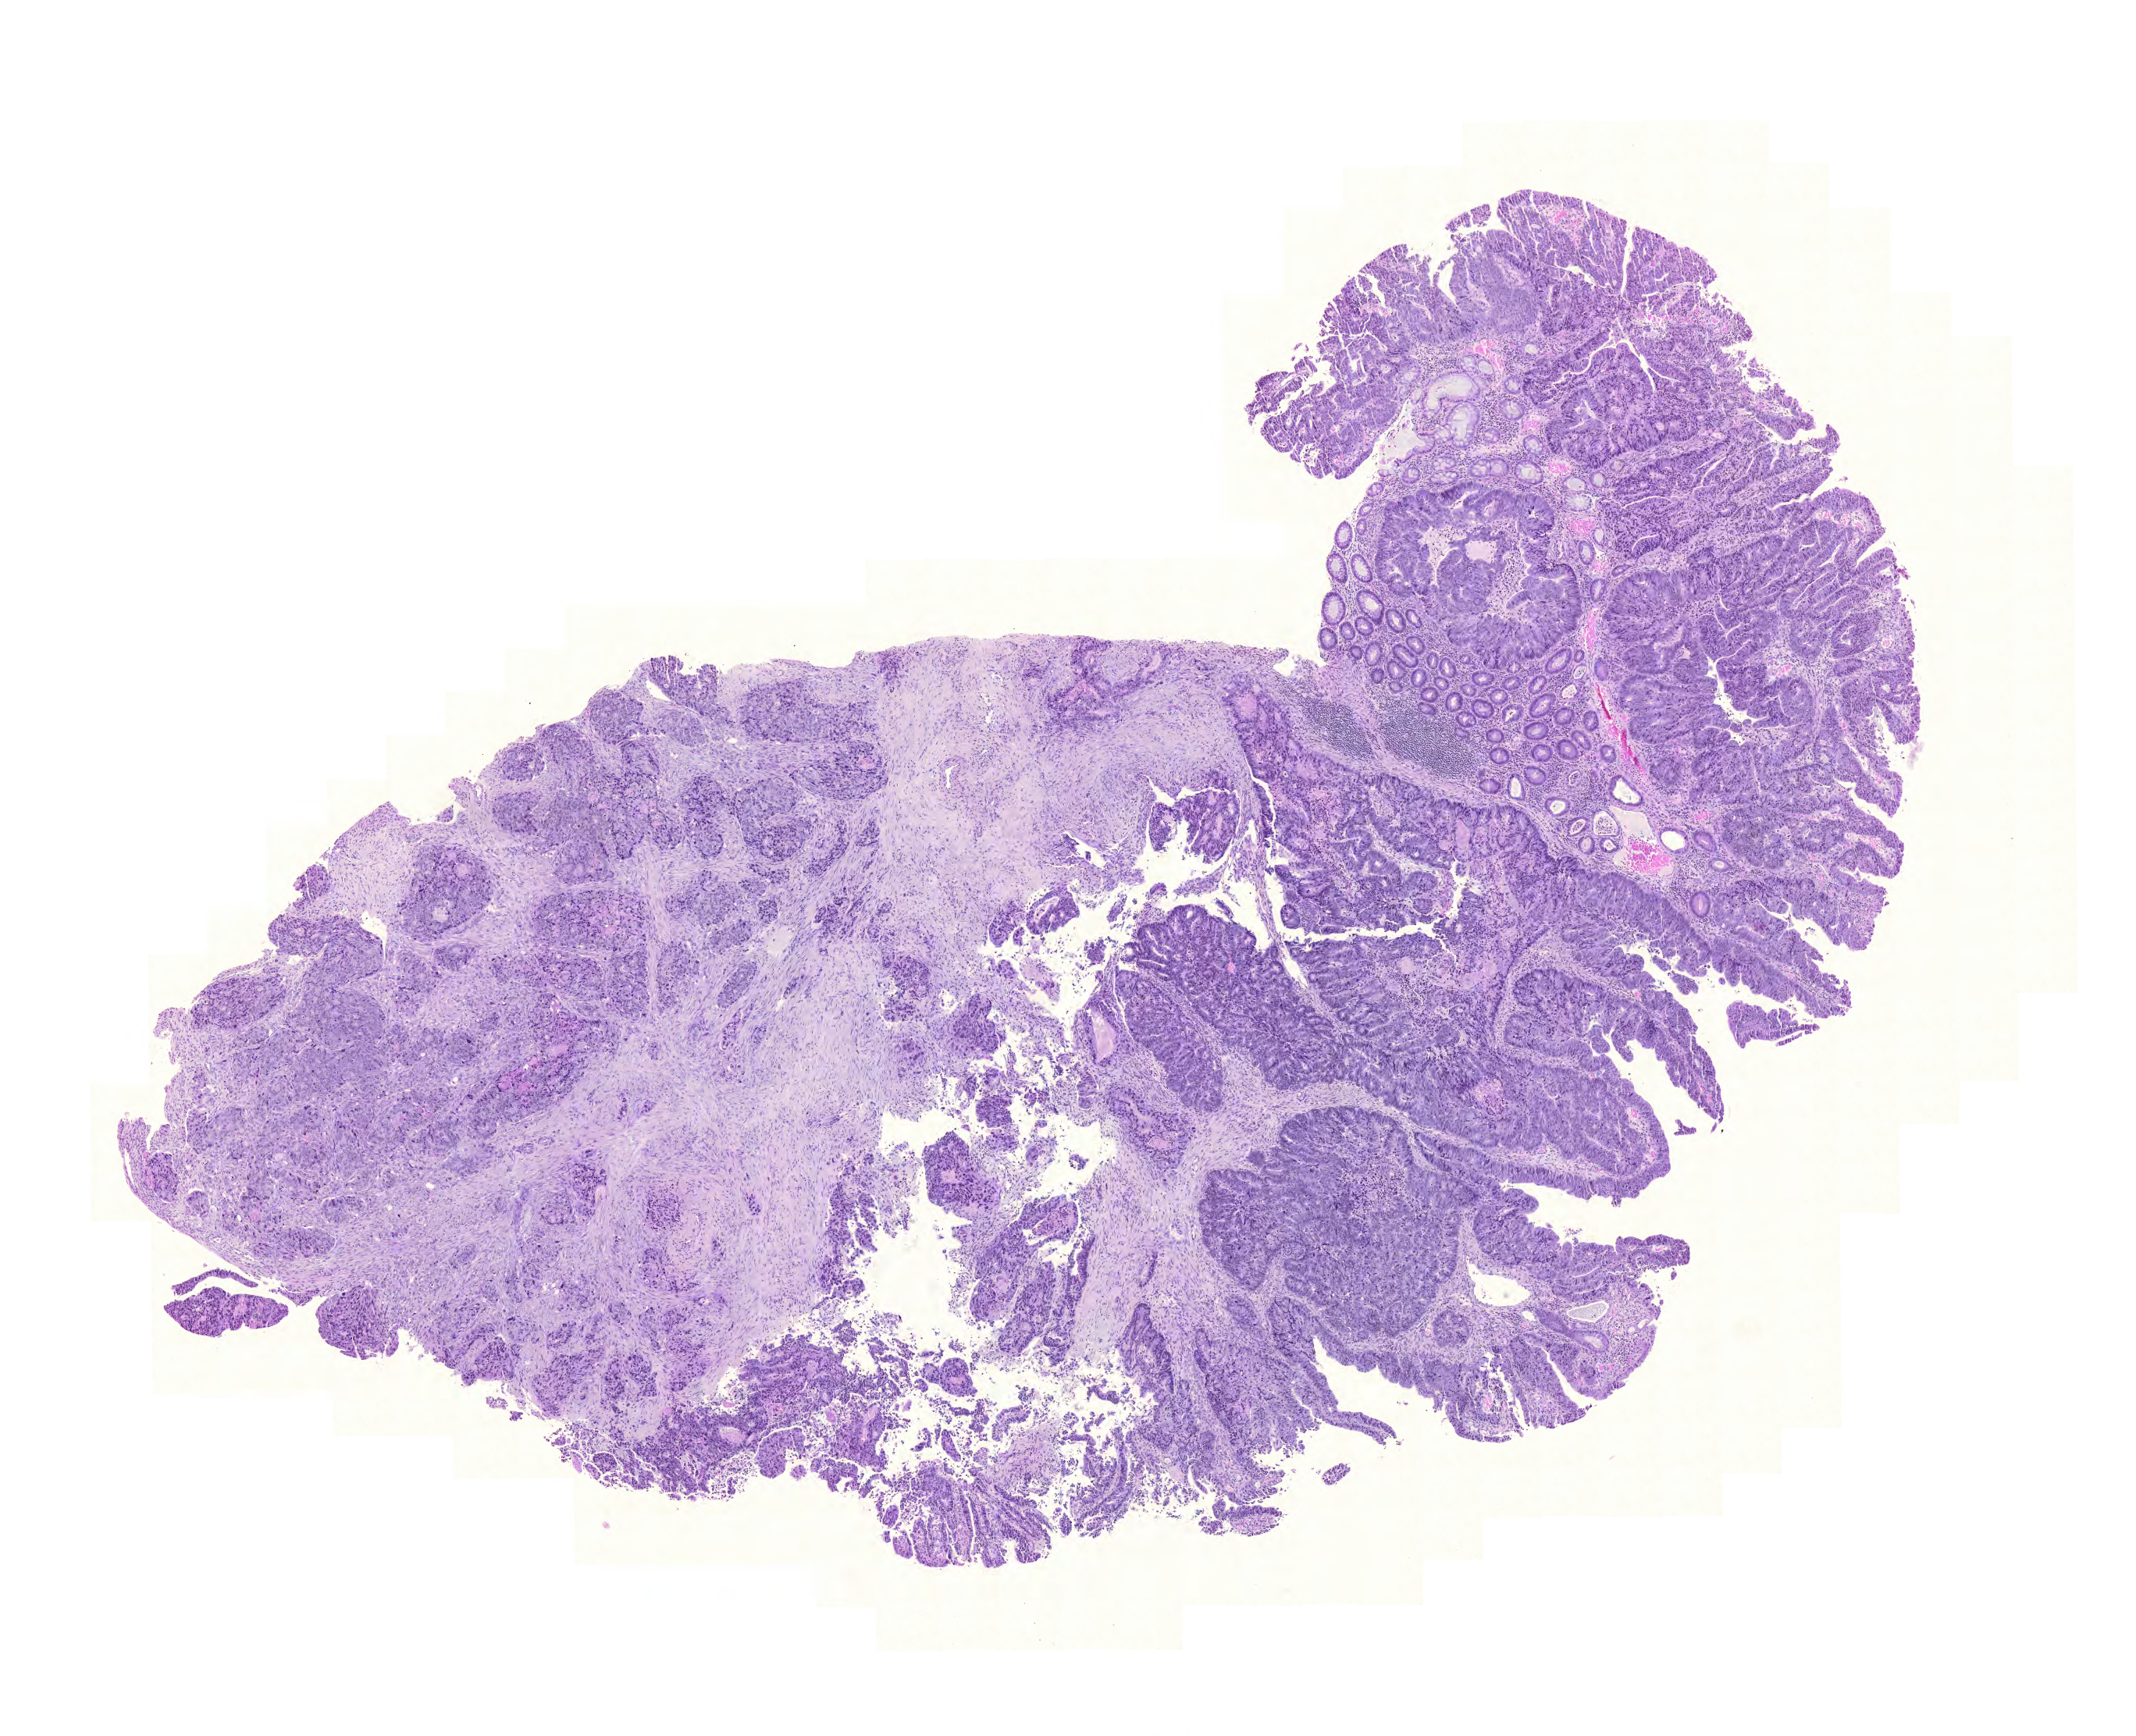
H&E-stained whole-slide image, a low-resolution overview of the entire scanned area, about 10.2 x 8.3 mm (from a 20x scan). Formalin-fixed paraffin-embedded (FFPE) diagnostic section. Sample: primary tumour, colon. Male, age 73 years at initial diagnosis.
Pathologic diagnosis: Adenocarcinoma, NOS. Lymph nodes positive (case pathology): 4 of 24 examined. AJCC pathologic stage: IV (6th edition).